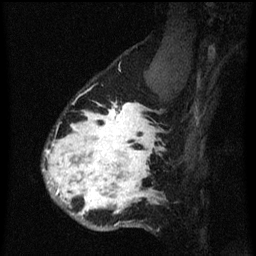
Breast MRI (dynamic contrast-enhanced), one sagittal slice; position 47 of 60 along the scan axis; dynamic contrast-enhanced series, image 2 of 3 at this slice position (ordered by acquisition); 1.5 T; TE 4.2 ms, TR 8.4 ms; 2 mm slice thickness; 256 × 256 image matrix, field of view 180 × 180 mm. Female patient, age 34 years. From the clinical record (not read from this slice): setting: breast cancer imaged before/during neoadjuvant chemotherapy; receptor status: HR-positive, HER2-negative.
Outlined on this slice (semi-automatic segmentation, software-assisted and operator-edited):
- analysis volume of interest (the breast-tissue region the enhancement analysis was run in; not a lesion): bounding box <44,58,173,231> (left, top, right, bottom; pixels)
- tumour enhancement mask (voxels above the 70 % enhancement threshold inside the analysis volume of interest): <46,102,157,217>